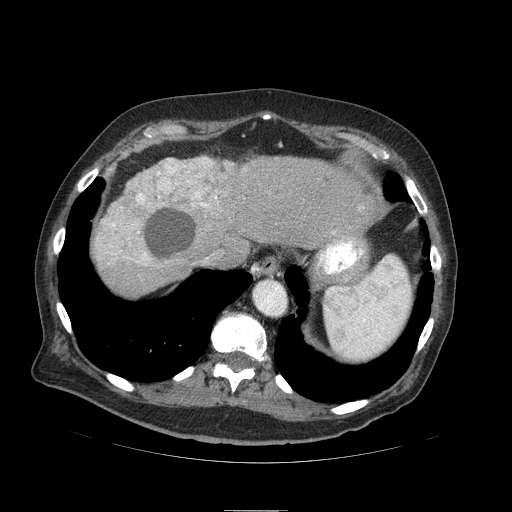
Contrast-enhanced abdominal CT (liver protocol), one axial slice; slice 76 of 103 in the series (ordered by position); 120 kVp; soft-tissue window (W 400 / L 40 HU); 2.5 mm slice thickness; 512 × 512 image matrix, field of view 440 × 440 mm. Case-level facts recorded for this patient, not image findings: diagnosis: hepatocellular carcinoma (patient treated with transarterial chemoembolisation; whether this scan precedes or follows treatment is not stated here); TNM stage (as recorded): Stage-IIIA; Child-Pugh class: B; tumour nodularity: multinodular; tumour size: 13 cm.
Outlined on this slice (semi-automatically segmented with operator editing):
- liver parenchyma outside the tumour (the mass and vessels are separate outlines, so this box may not span the whole liver): bounding box [x1, y1, x2, y2] px = [92, 156, 382, 294]
- mass: [95, 155, 255, 267]